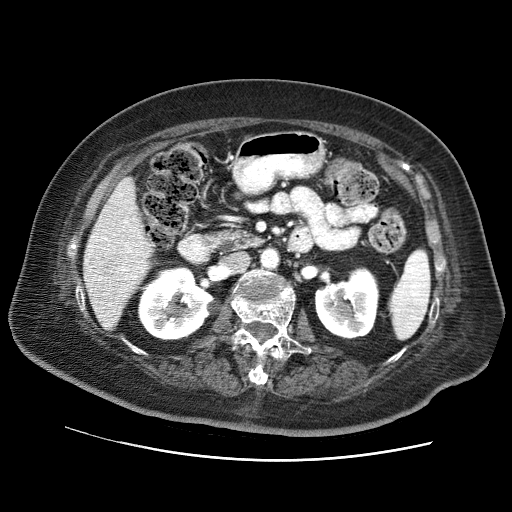
Contrast-enhanced abdominal CT (liver protocol), one axial slice; position 26 of 73 along the scan axis; reconstruction kernel STANDARD; 120 kVp; soft-tissue window (W 400 / L 40 HU); 2.5 mm slice thickness; 512 × 512 image matrix, field of view 380 × 380 mm. Case-level facts recorded for this patient, not image findings: diagnosis: hepatocellular carcinoma (patient treated with transarterial chemoembolisation; whether this scan precedes or follows treatment is not stated here); TNM stage (as recorded): Stage-I; Child-Pugh class: A.
Outlined on this slice (semi-automatically segmented with operator editing):
- liver parenchyma outside the tumour (the mass and vessels are separate outlines, so this box may not span the whole liver): bounding box [x1, y1, x2, y2] px = [84, 177, 152, 328]
- liver vessels: [86, 193, 144, 306]